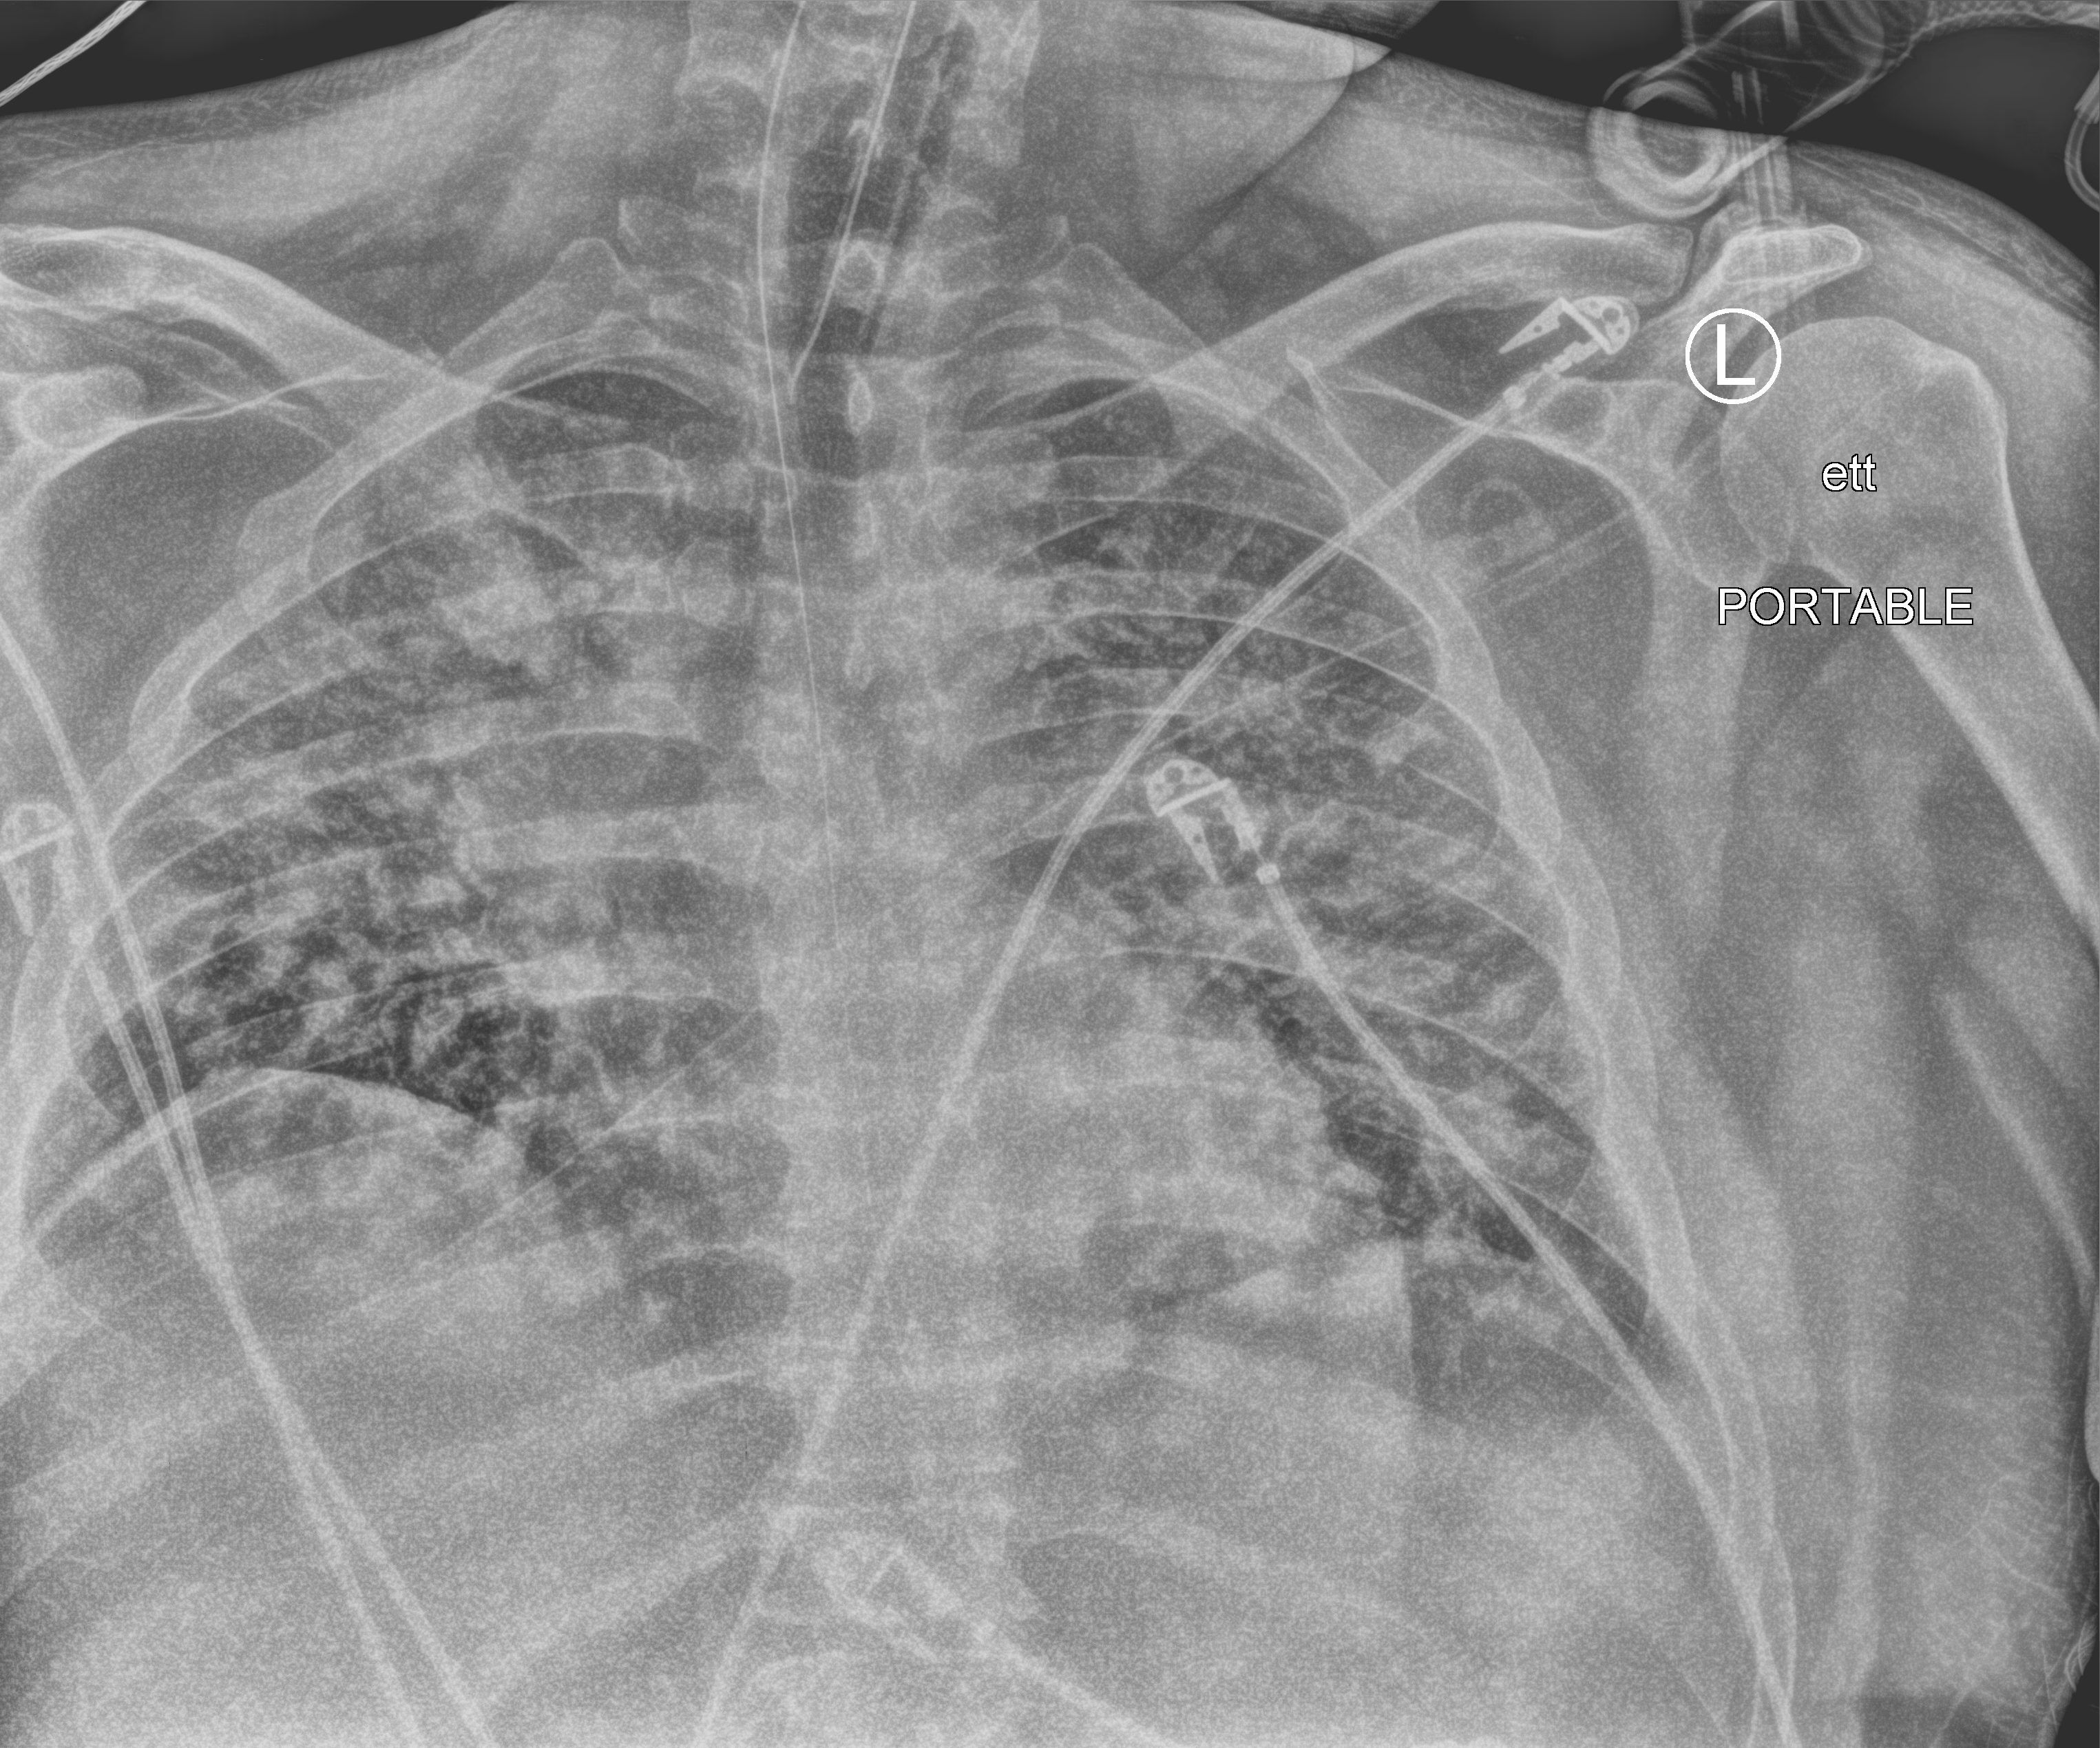
Portable chest radiograph; anteroposterior (AP) projection. Patient hospitalised with COVID-19, aged 18–59 years.
Hospital-stay facts (about this admission, not read from this image; timing relative to this image not recorded): admitted to intensive care during this hospital stay: yes; mechanically ventilated during this hospital stay: yes.